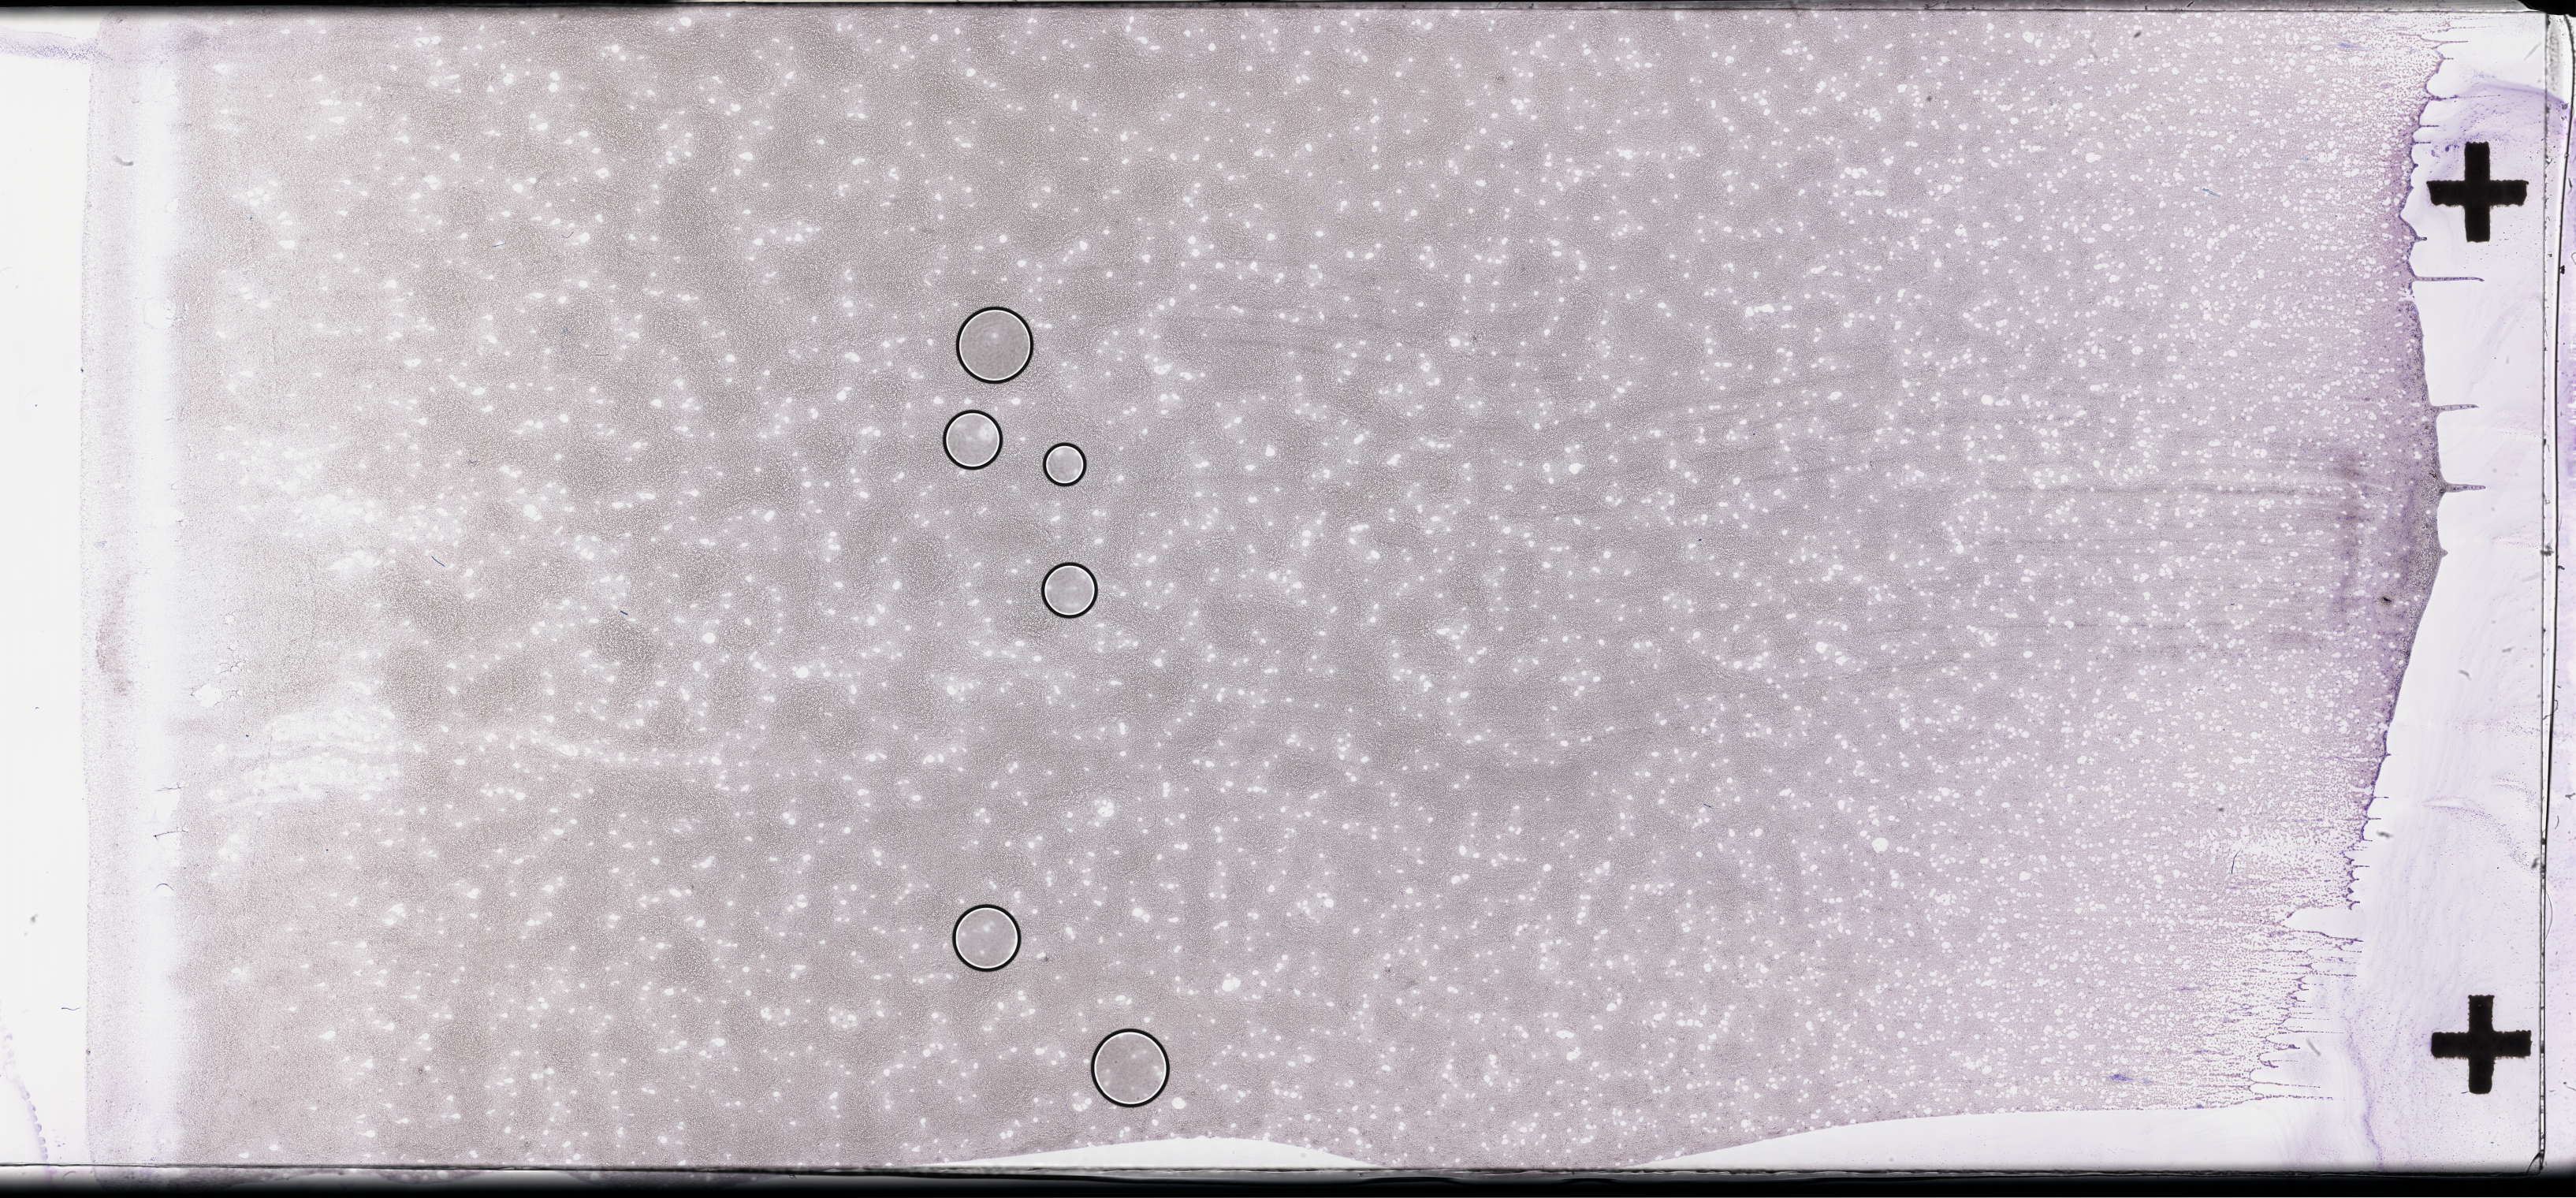
Whole-slide image of a whole blood smear, Wright-Giemsa stain — shown as a low-resolution overview of the whole scanned area (about 52.8 x 24.5 mm), smear from an EDTA sample, collected on treatment. Patient: female.
* patient diagnosis: Plasma Cell Myeloma